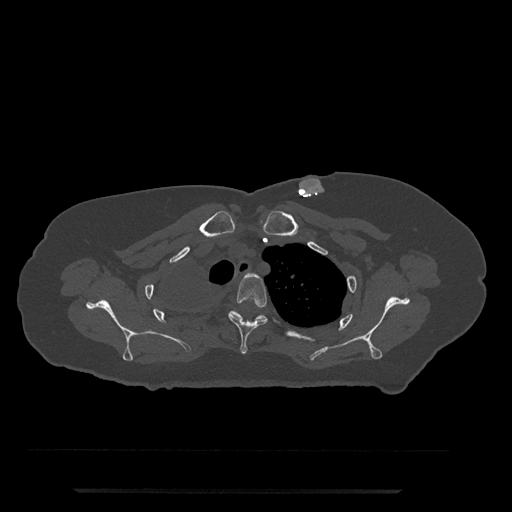
CT including the spine, one axial slice. 120 kVp. Bone window (W 1800 / L 400 HU). 512 × 512 image matrix, field of view 440 × 440 mm. Female patient, age 51 years. From the clinical record (not read from this slice): primary cancer: neuro; vertebrae with lytic lesions (as recorded): T8.
Outlined on this slice (semi-automatically segmented with operator editing):
- T3 vertebra: bounding box (x1, y1, x2, y2) in pixels: (228, 273, 268, 354)
- T4 vertebra: (229, 311, 266, 320)